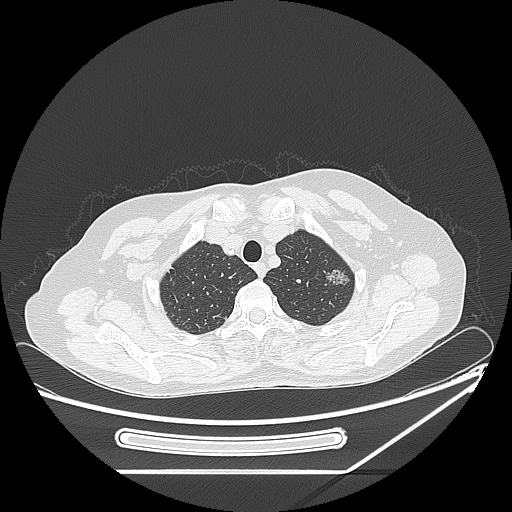
Chest CT, one axial slice. Position 208 of 250 along the scan axis. Lung window (W 1500 / L -600 HU). 512 × 512 image matrix. Female patient, age 57 years. Case-level facts recorded for this patient, not image findings: clinical TNM (as recorded): T1c N0 M0.
Structures marked on this image (bounding box drawn by a radiologist):
- lung tumour (recorded histology: adenocarcinoma): bounding box (x1, y1, x2, y2) in pixels: (320, 266, 351, 299)